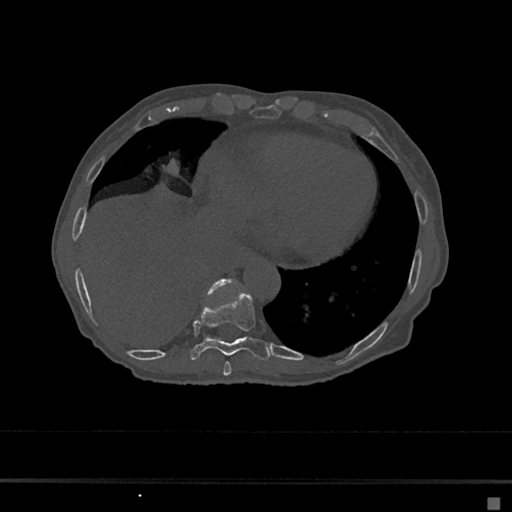
CT including the spine, one axial slice. Slice 270 of 797 in the series (ordered by position). 120 kVp. Bone window (W 1800 / L 400 HU). 0.5 mm slice thickness. 512 × 512 image matrix, field of view 360 × 360 mm. Patient: female, 68 years. From the clinical record (not read from this slice): primary cancer: renal.
Annotated regions visible in this slice (semi-automatic segmentation, software-assisted and operator-edited):
- T10 vertebra: bounding box <207,280,231,295> (left, top, right, bottom; pixels)
- T8 vertebra: <223,362,232,377>
- T9 vertebra: <189,290,272,361>